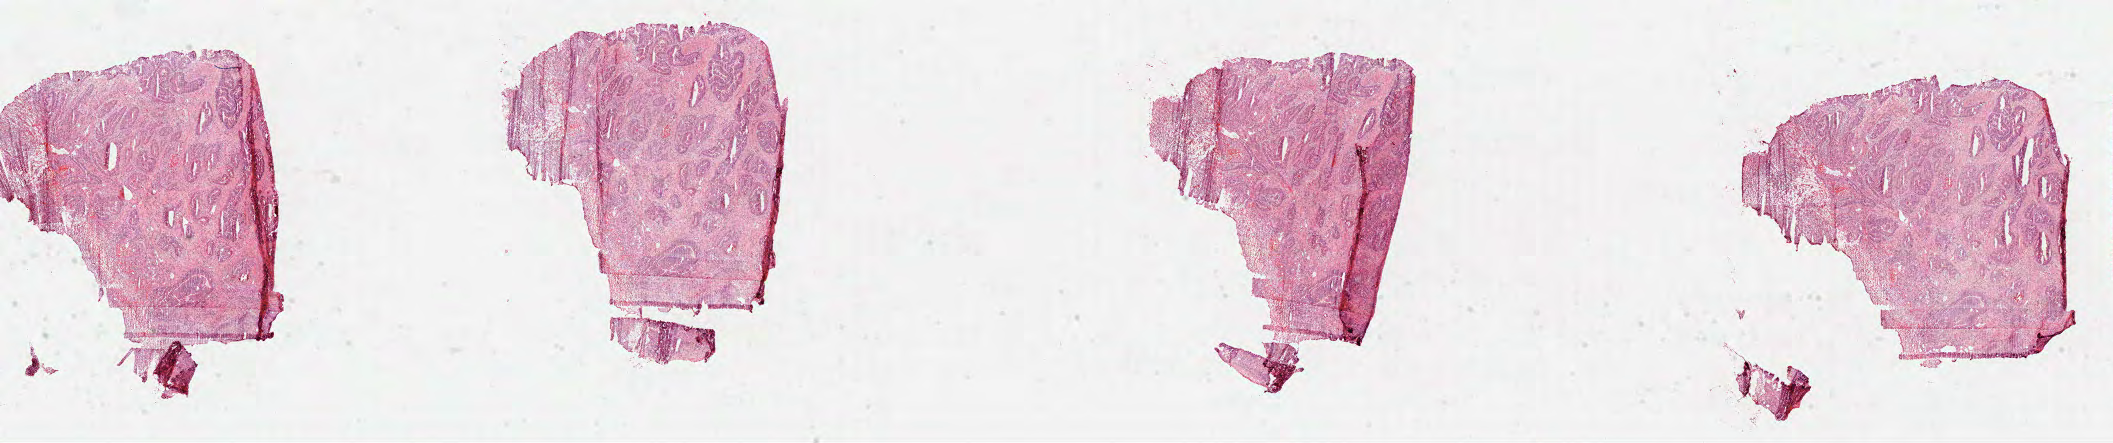
Digitized Hematoxylin and eosin (H&E) stained tissue section (whole slide) — low-resolution overview of the scanned area, about 34.1 x 7.1 mm. FFPE section. Primary tumour sample from the colon. Patient: female, age at initial diagnosis 51 years.
AJCC pathologic stage: I (7th edition). Pathologic diagnosis: Adenocarcinoma, NOS.